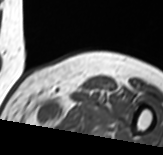
MRI of an extremity soft-tissue mass, one axial slice; position 53 of 65 along the scan axis; MR volume resampled by the dataset authors to the PET/CT grid (not the native acquisition matrix); 3.27 mm slice thickness; 163 × 155 image matrix, field of view 159 × 151 mm. Female patient. Case-level facts recorded for this patient, not image findings: histological type: pleomorphic leiomyosarcoma; grade: high; site of the primary tumour: left thigh.
Structures marked on this image (expert contour drawn on MRI and transferred to this co-registered scan by the dataset authors):
- gross tumour volume including surrounding oedema: bounding box (x1, y1, x2, y2) in pixels: (37, 97, 84, 121)